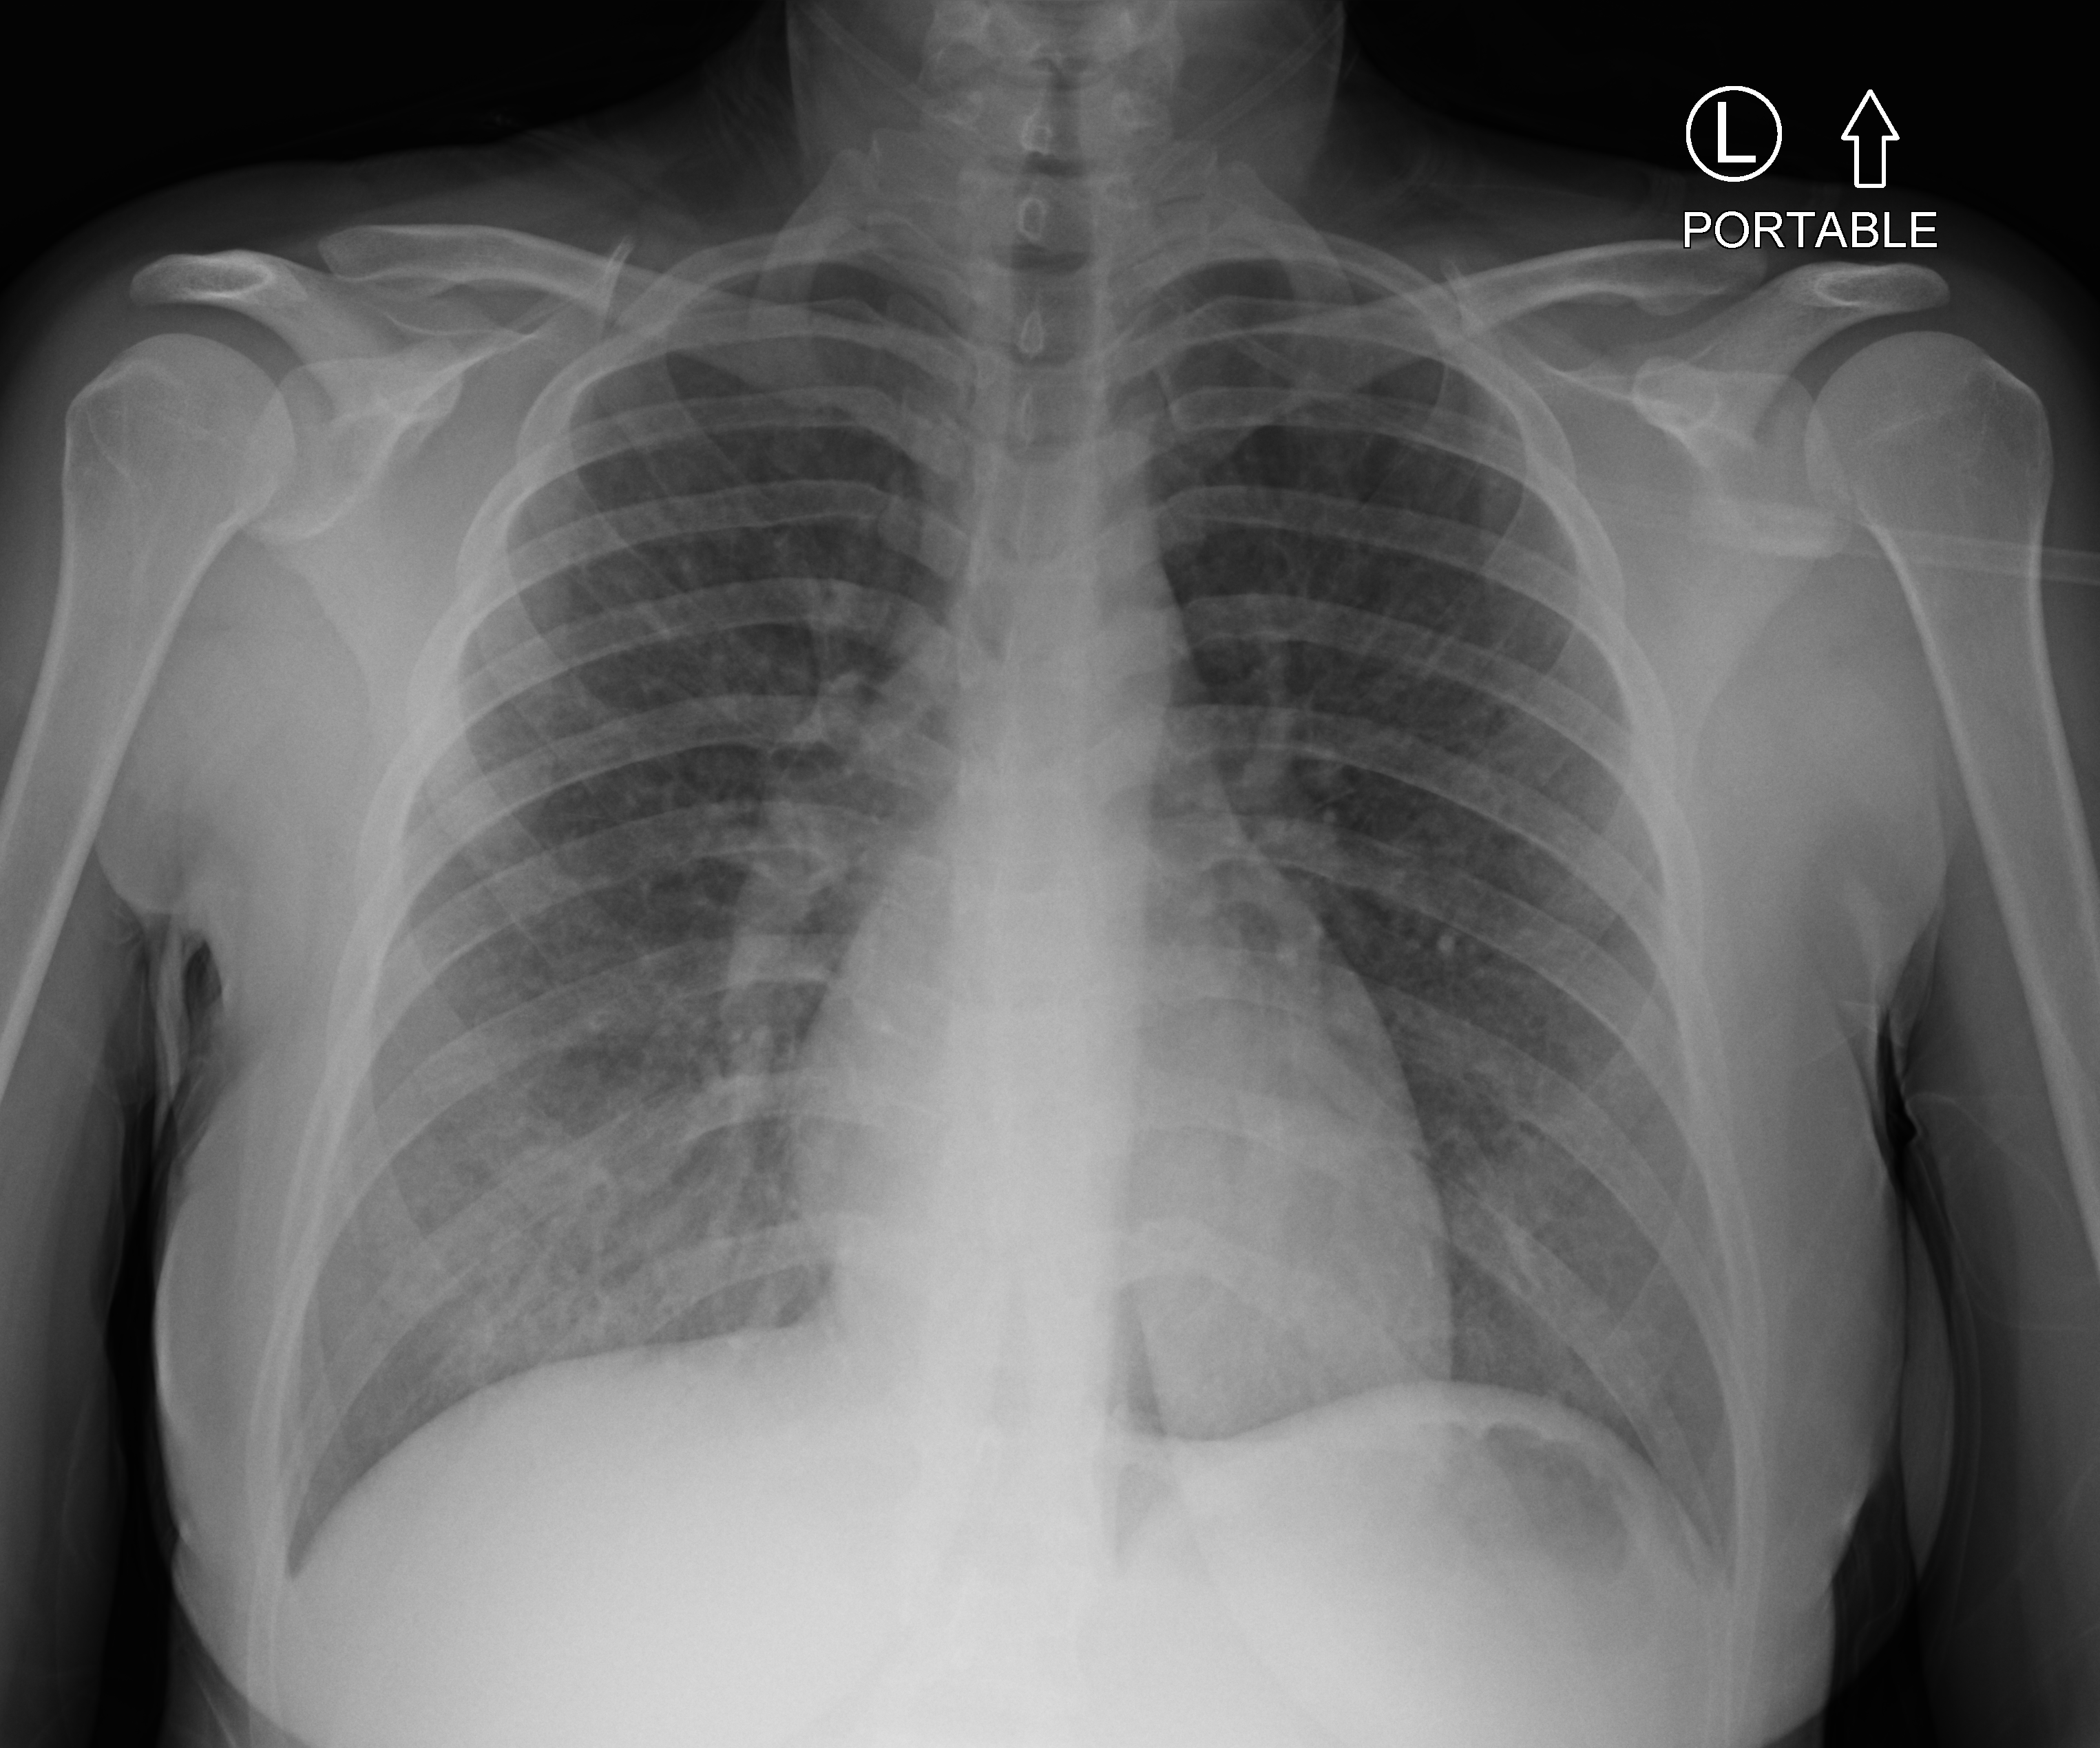
Bedside chest radiograph (computed radiography), anteroposterior (AP) projection. Patient hospitalised with COVID-19; female, aged 18–59 years.
Hospital-stay facts (about this admission, not read from this image; timing relative to this image not recorded): length of hospital stay: 3 days; admitted to intensive care during this hospital stay: no; mechanically ventilated during this hospital stay: no.